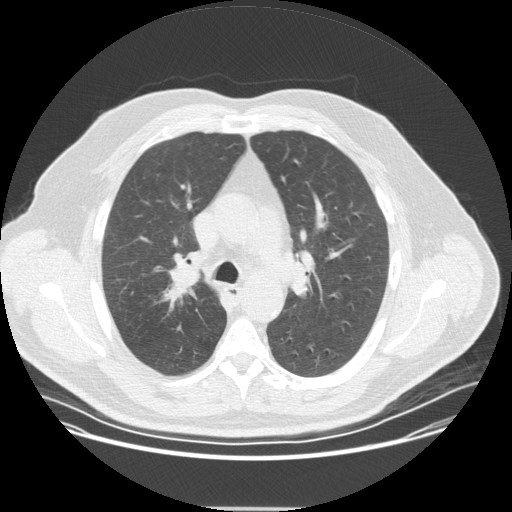
Low-dose screening chest CT, one axial slice; position 233 of 351 along the scan axis; reconstruction kernel STANDARD; lung window (W 1500 / L -600 HU); 2.5 mm slice thickness; 512 × 512 image matrix, field of view 419 × 419 mm.
Outlined on this slice (expert manual segmentation):
- lesion 1 (tumor, upper lobe of right lung): bounding box <163,266,202,304> (left, top, right, bottom; pixels)